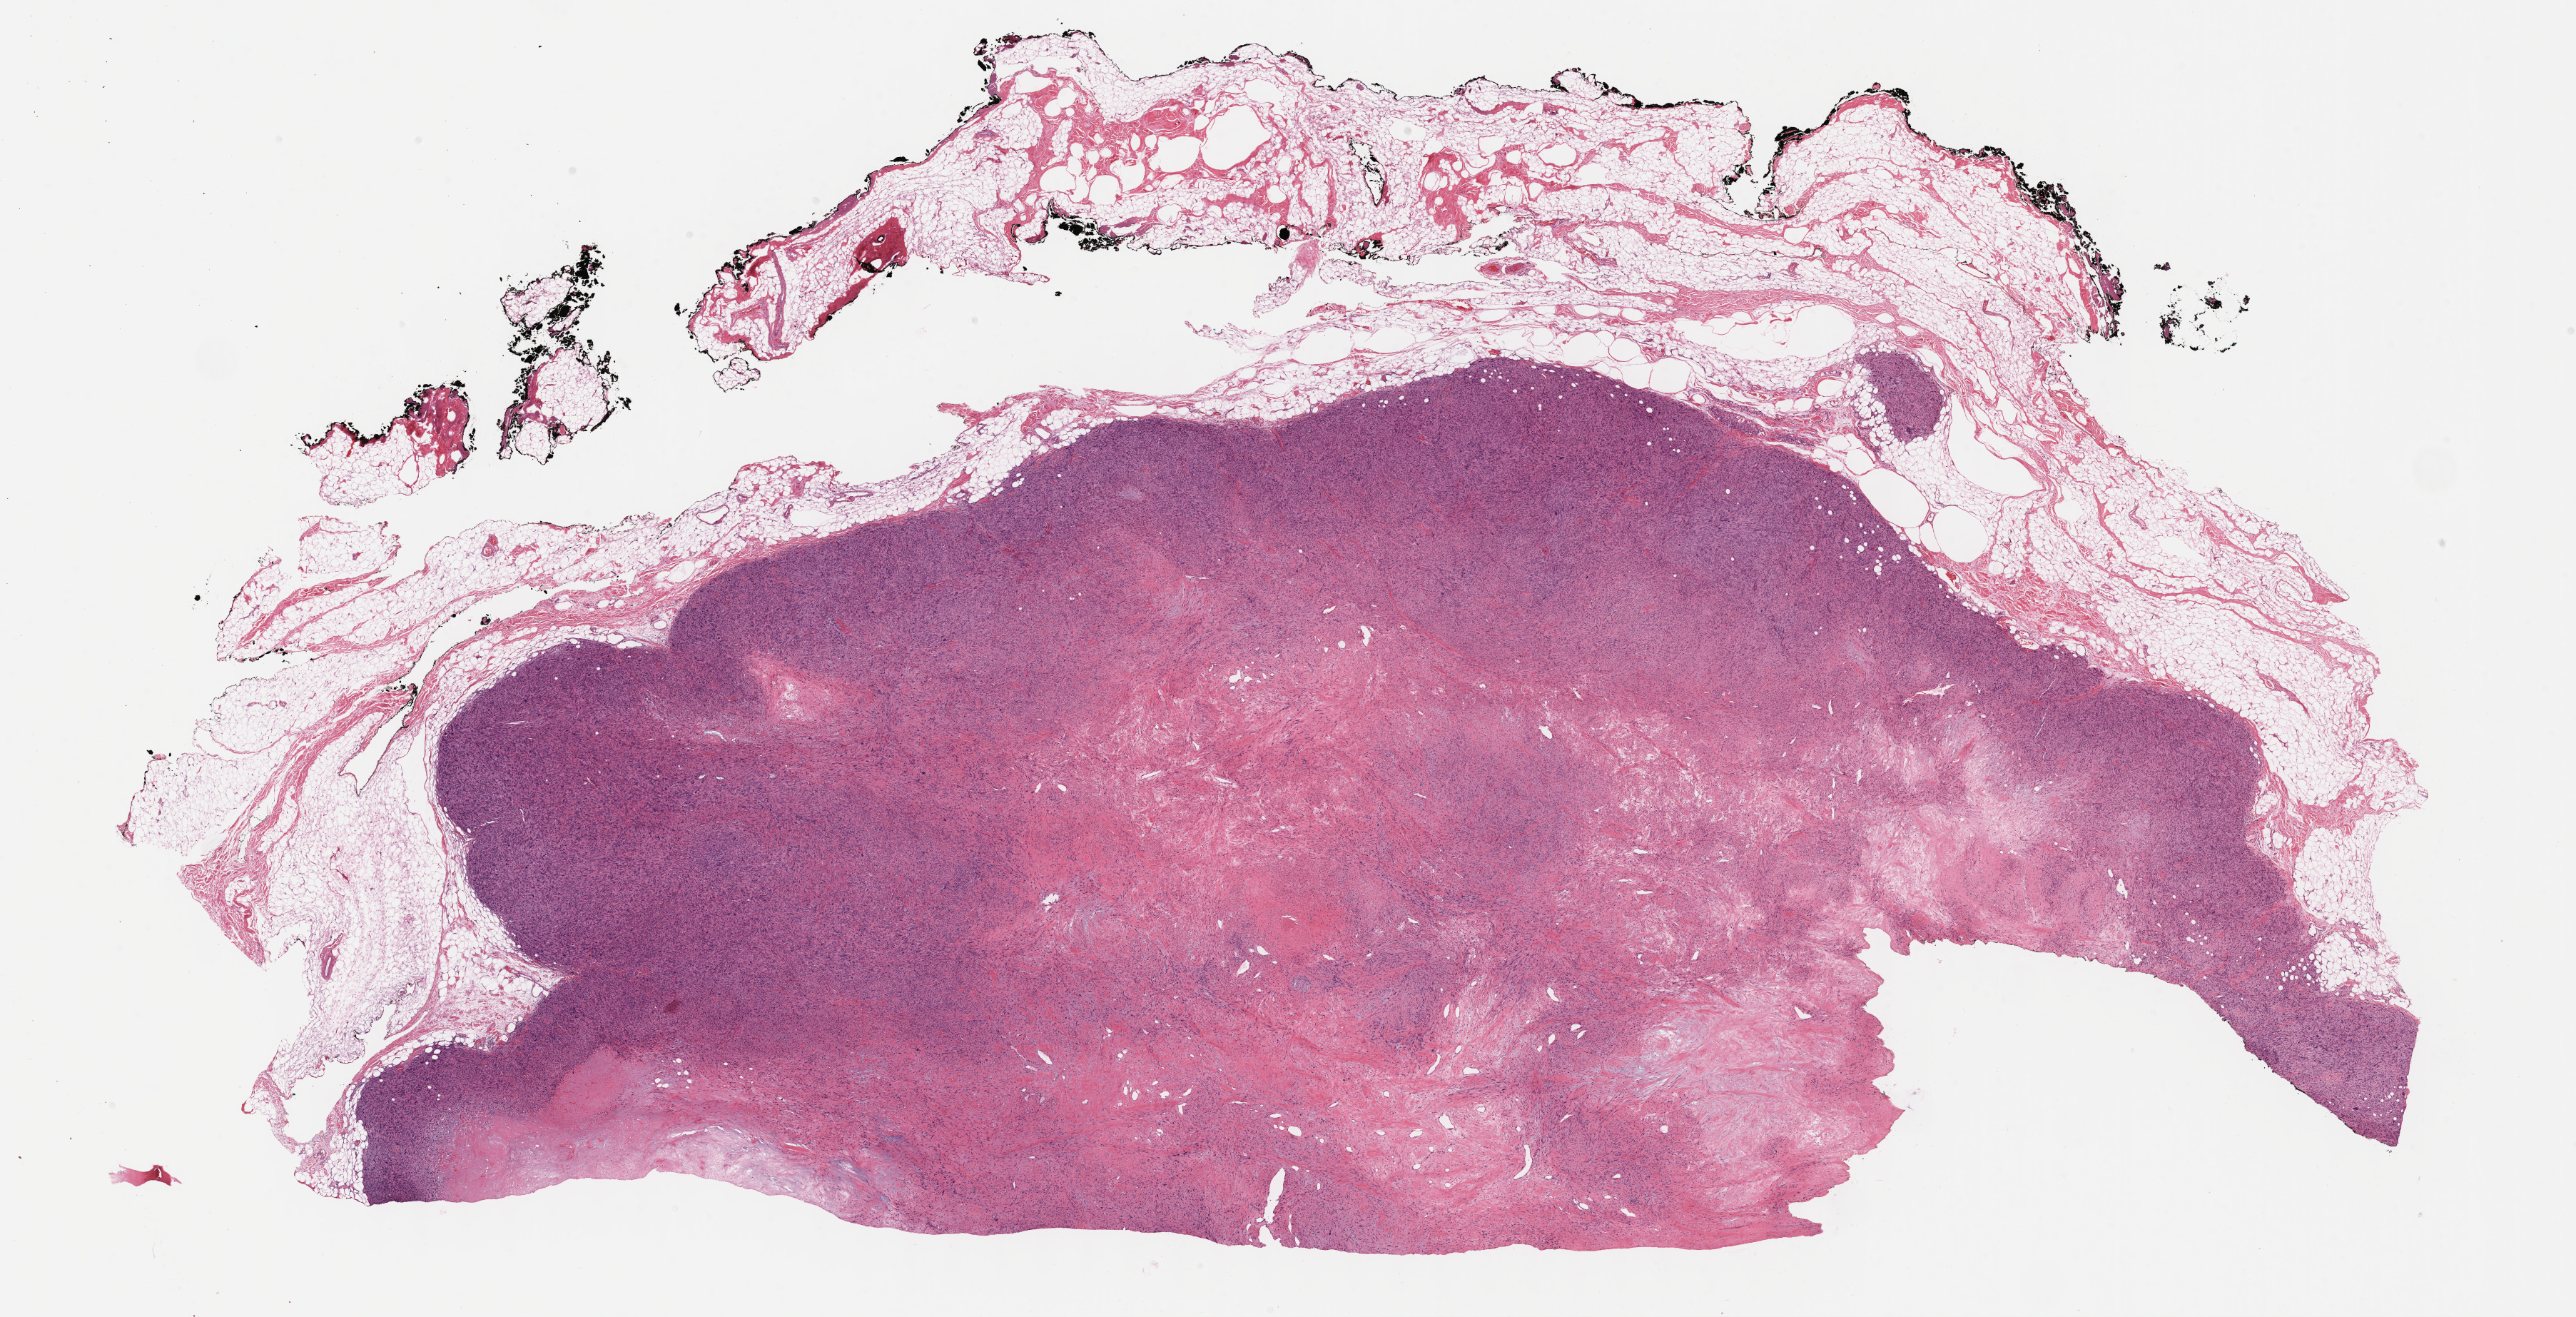
Whole-slide histology image, H&E-stained, a low-resolution overview of the entire scanned area, about 29.2 x 14.9 mm; FFPE section; connective, subcutaneous and other soft tissues, primary tumour sample. Female patient; age at initial diagnosis 52 years.
• pathologic diagnosis: Leiomyosarcoma, NOS (connective, subcutaneous and other soft tissues of upper limb and shoulder)